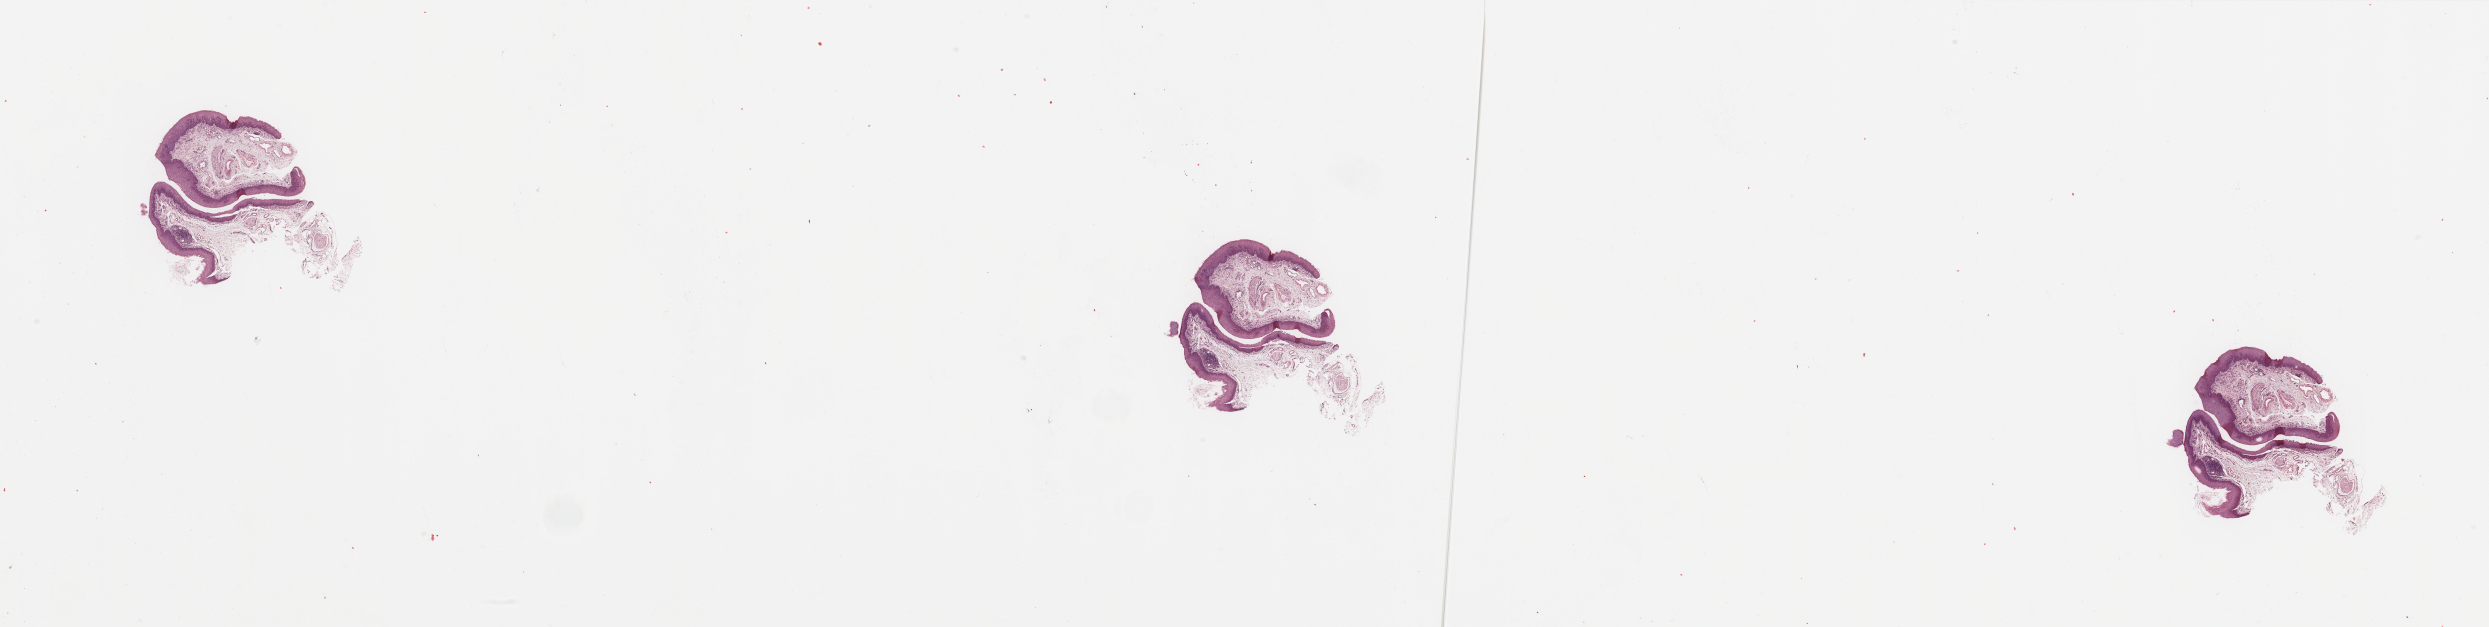
Whole-slide histology image, H&E — shown as a low-resolution overview of the whole scanned area (about 39.4 x 9.9 mm, slide scanned at 20x), head and neck, normal (non-tumour) tissue. 68-year-old male patient.
This section: normal (non-tumour) tissue from the same patient. Patient diagnosis: Squamous cell carcinoma, NOS (larynx, NOS).